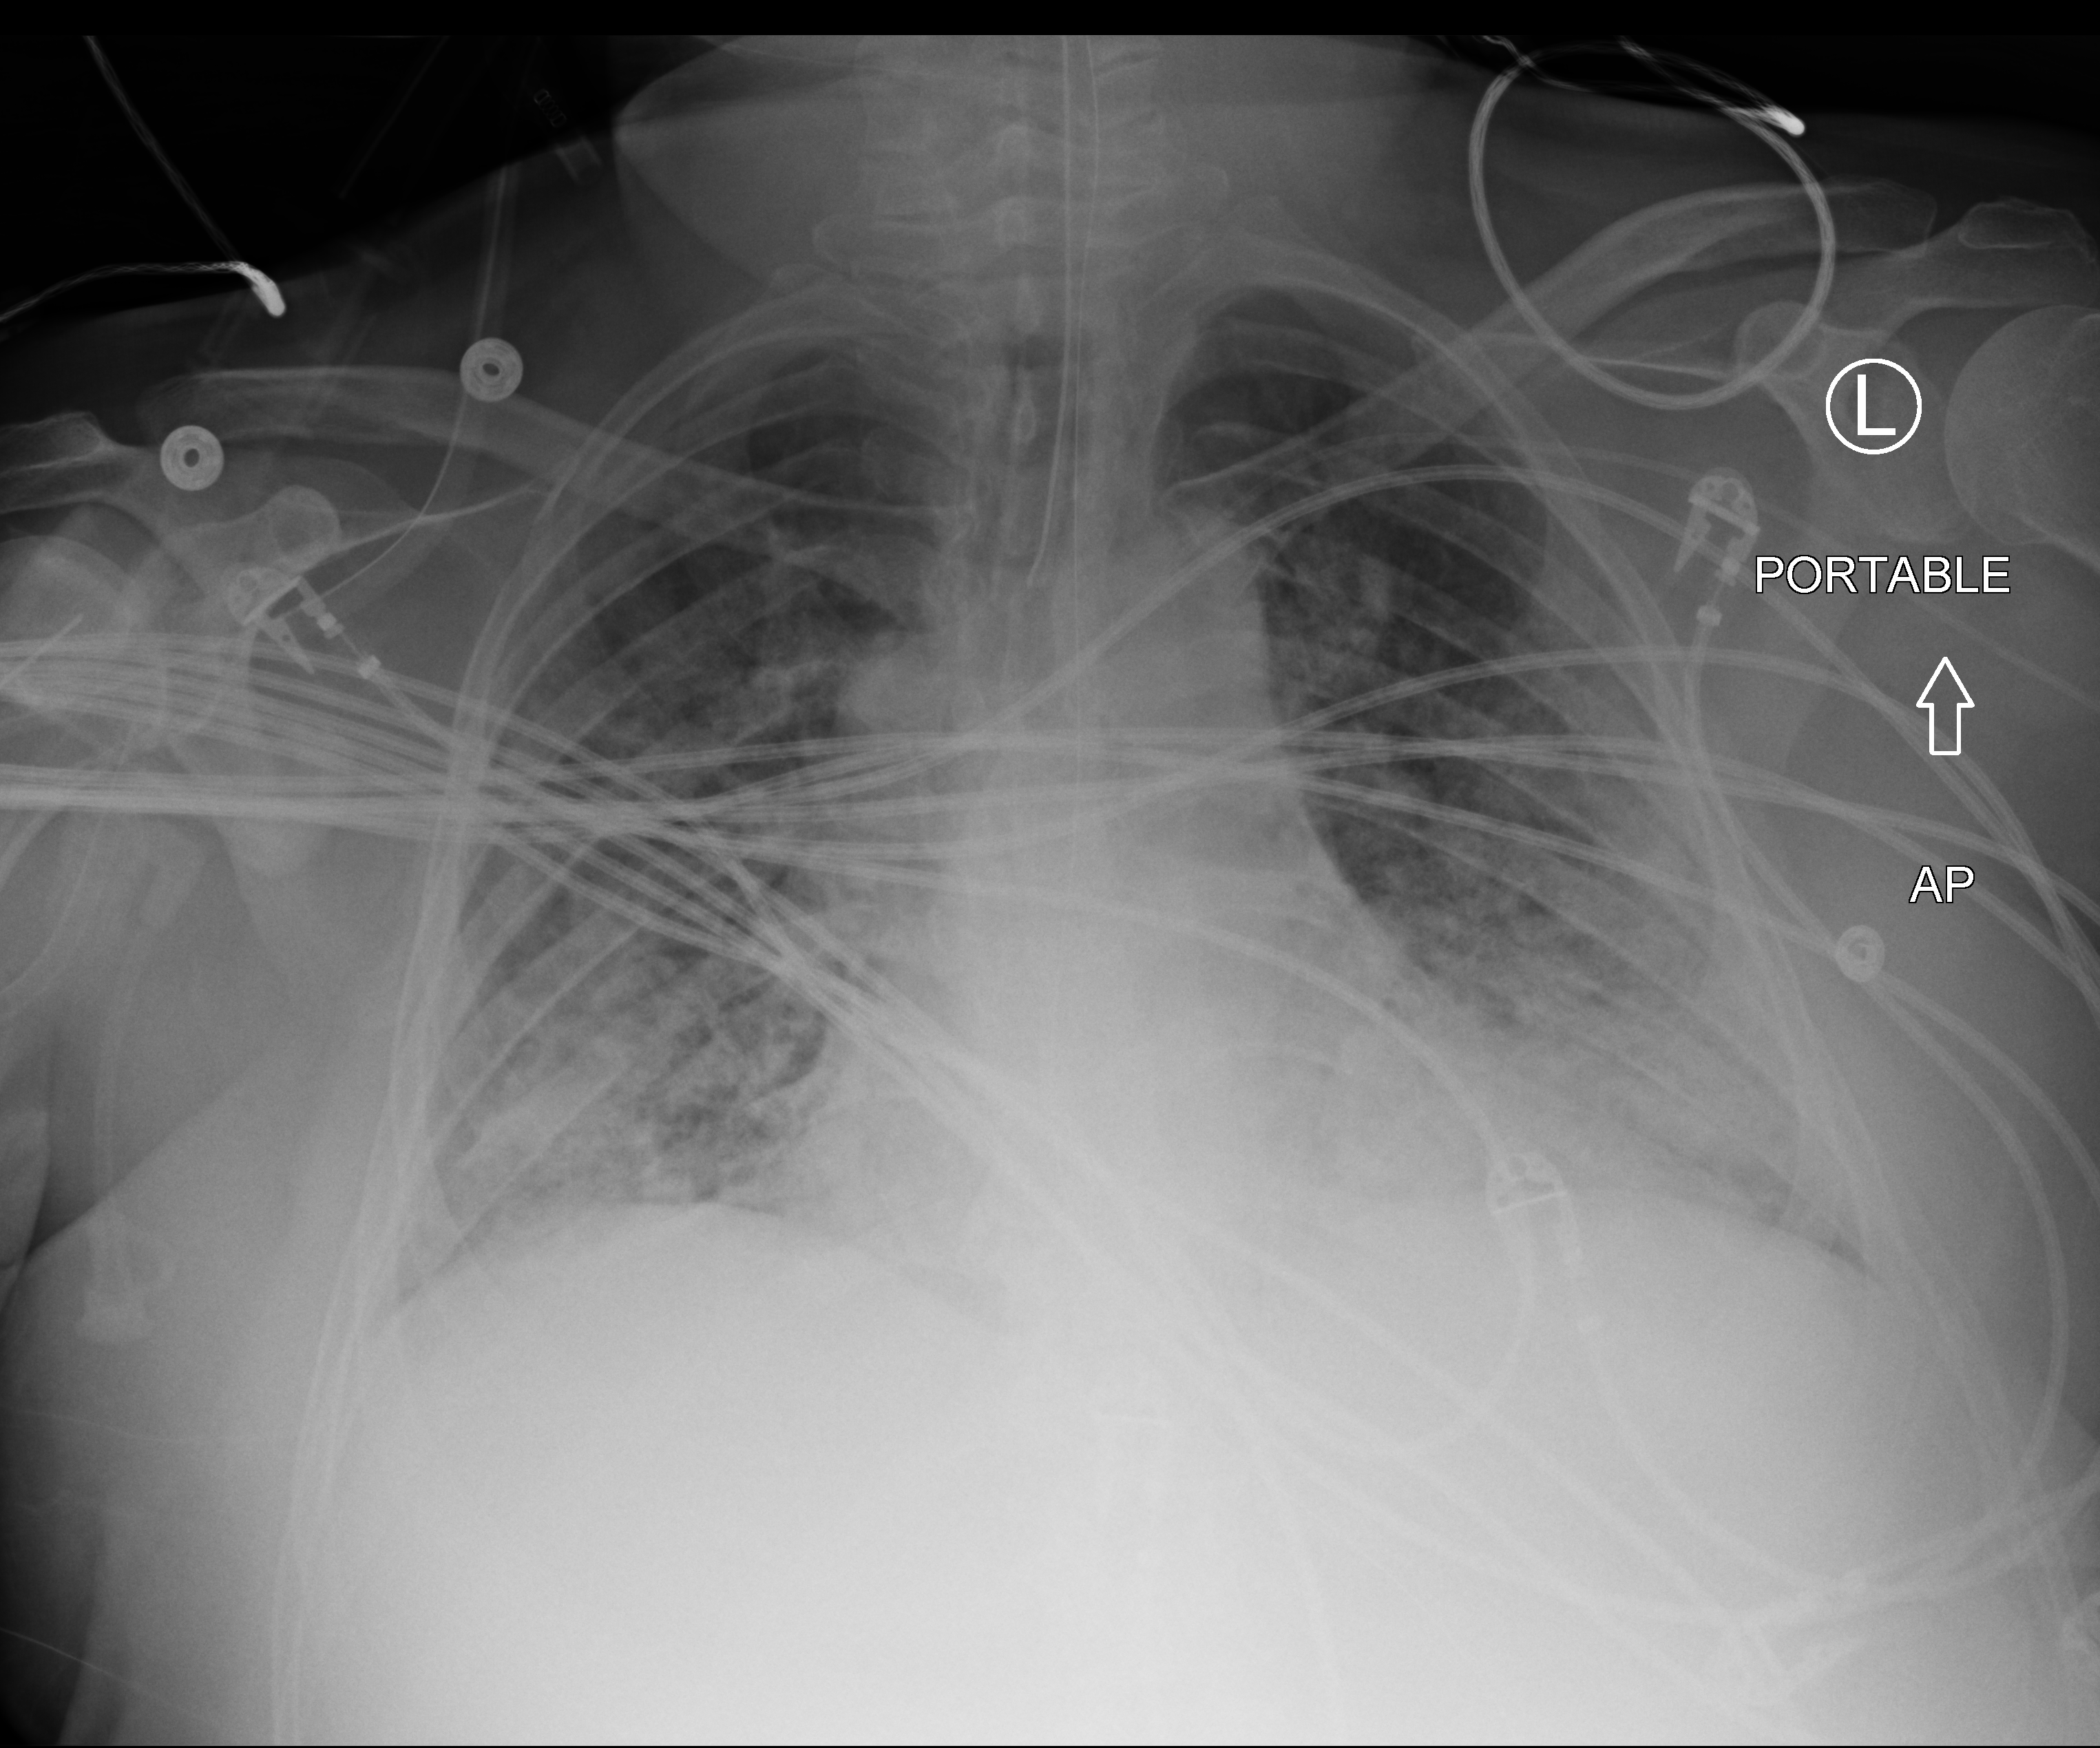
Bedside chest radiograph (computed radiography); anteroposterior (AP) projection. Patient hospitalised with COVID-19; male, aged 18–59 years.
From the hospital-stay record, not from the radiograph (when in the stay this image was taken is not recorded):
- admitted to intensive care during this hospital stay: yes
- smoking status (admission record): never
- mechanically ventilated during this hospital stay: yes